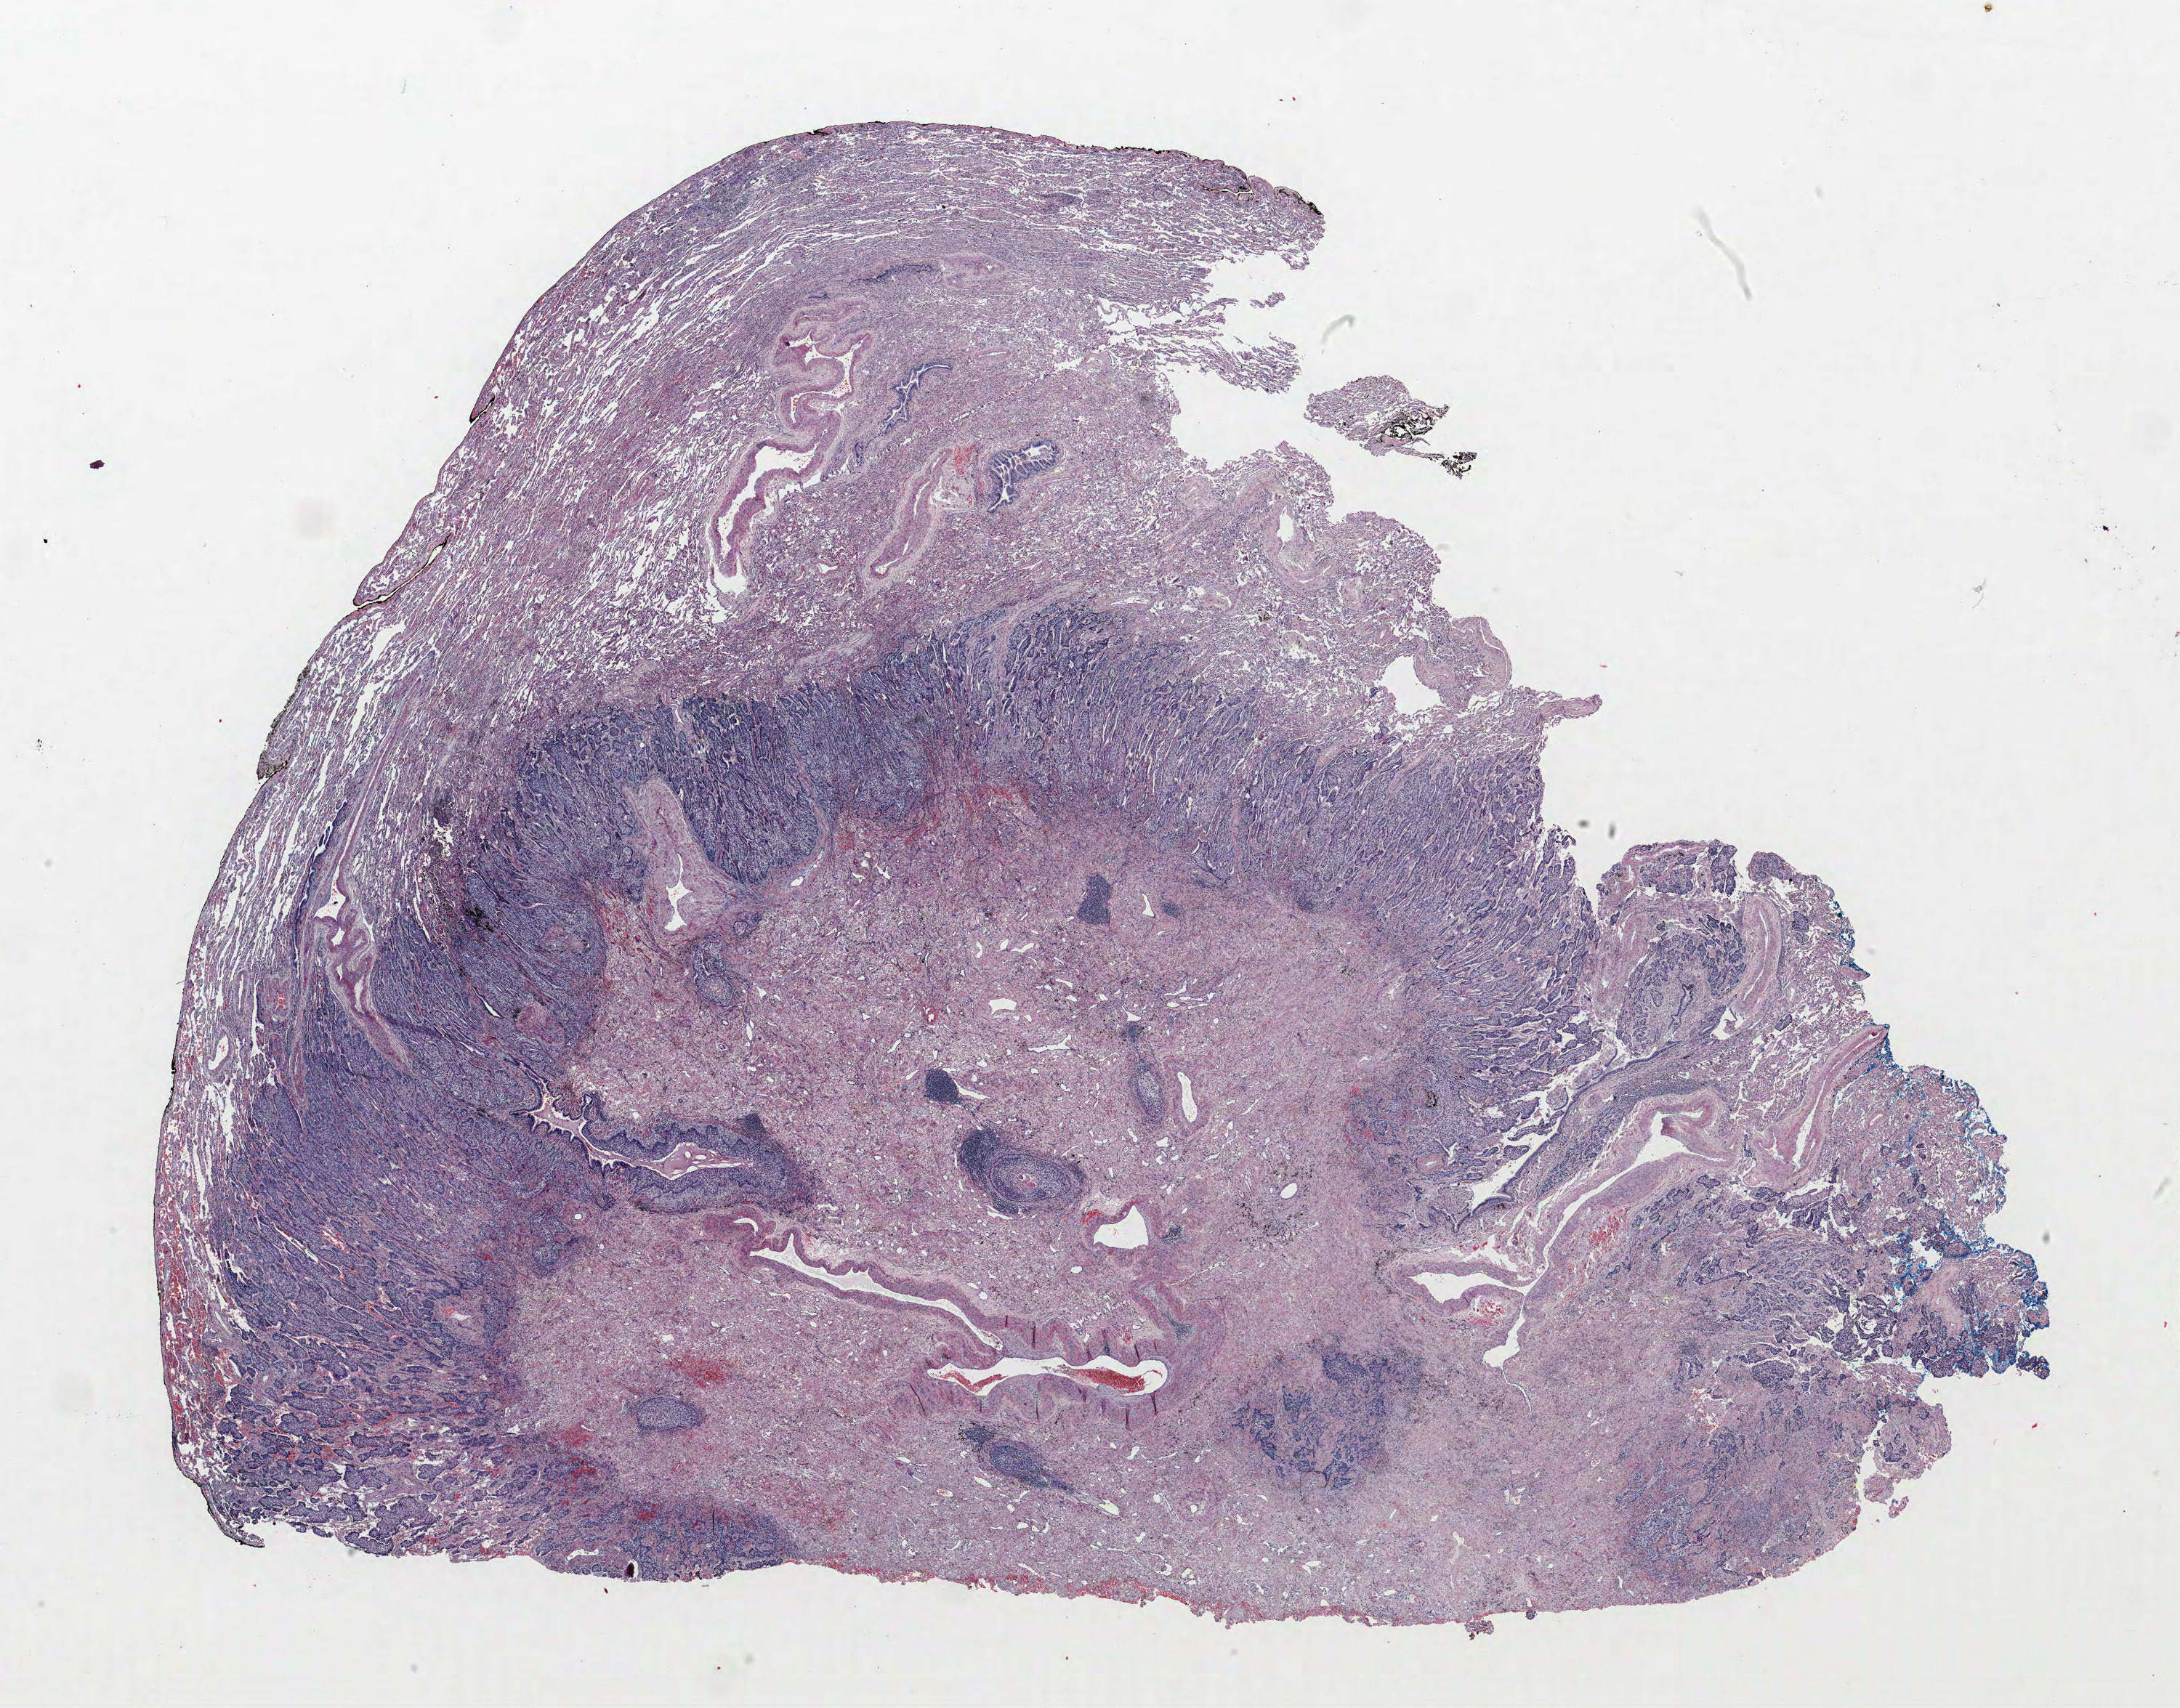
H&E-stained whole-slide image, low-resolution overview of the scanned area, about 24.0 x 18.8 mm. Formalin-fixed paraffin-embedded (FFPE) section. Lung. Male patient, aged 70 at enrolment. Grade: poorly differentiated (G3).
Participant's lung-cancer diagnosis: Squamous cell carcinoma, NOS. Tumour size (pathology): 24 mm. Primary tumour location (clinical record): right lower lobe. Stage (AJCC 6th edition): IB.